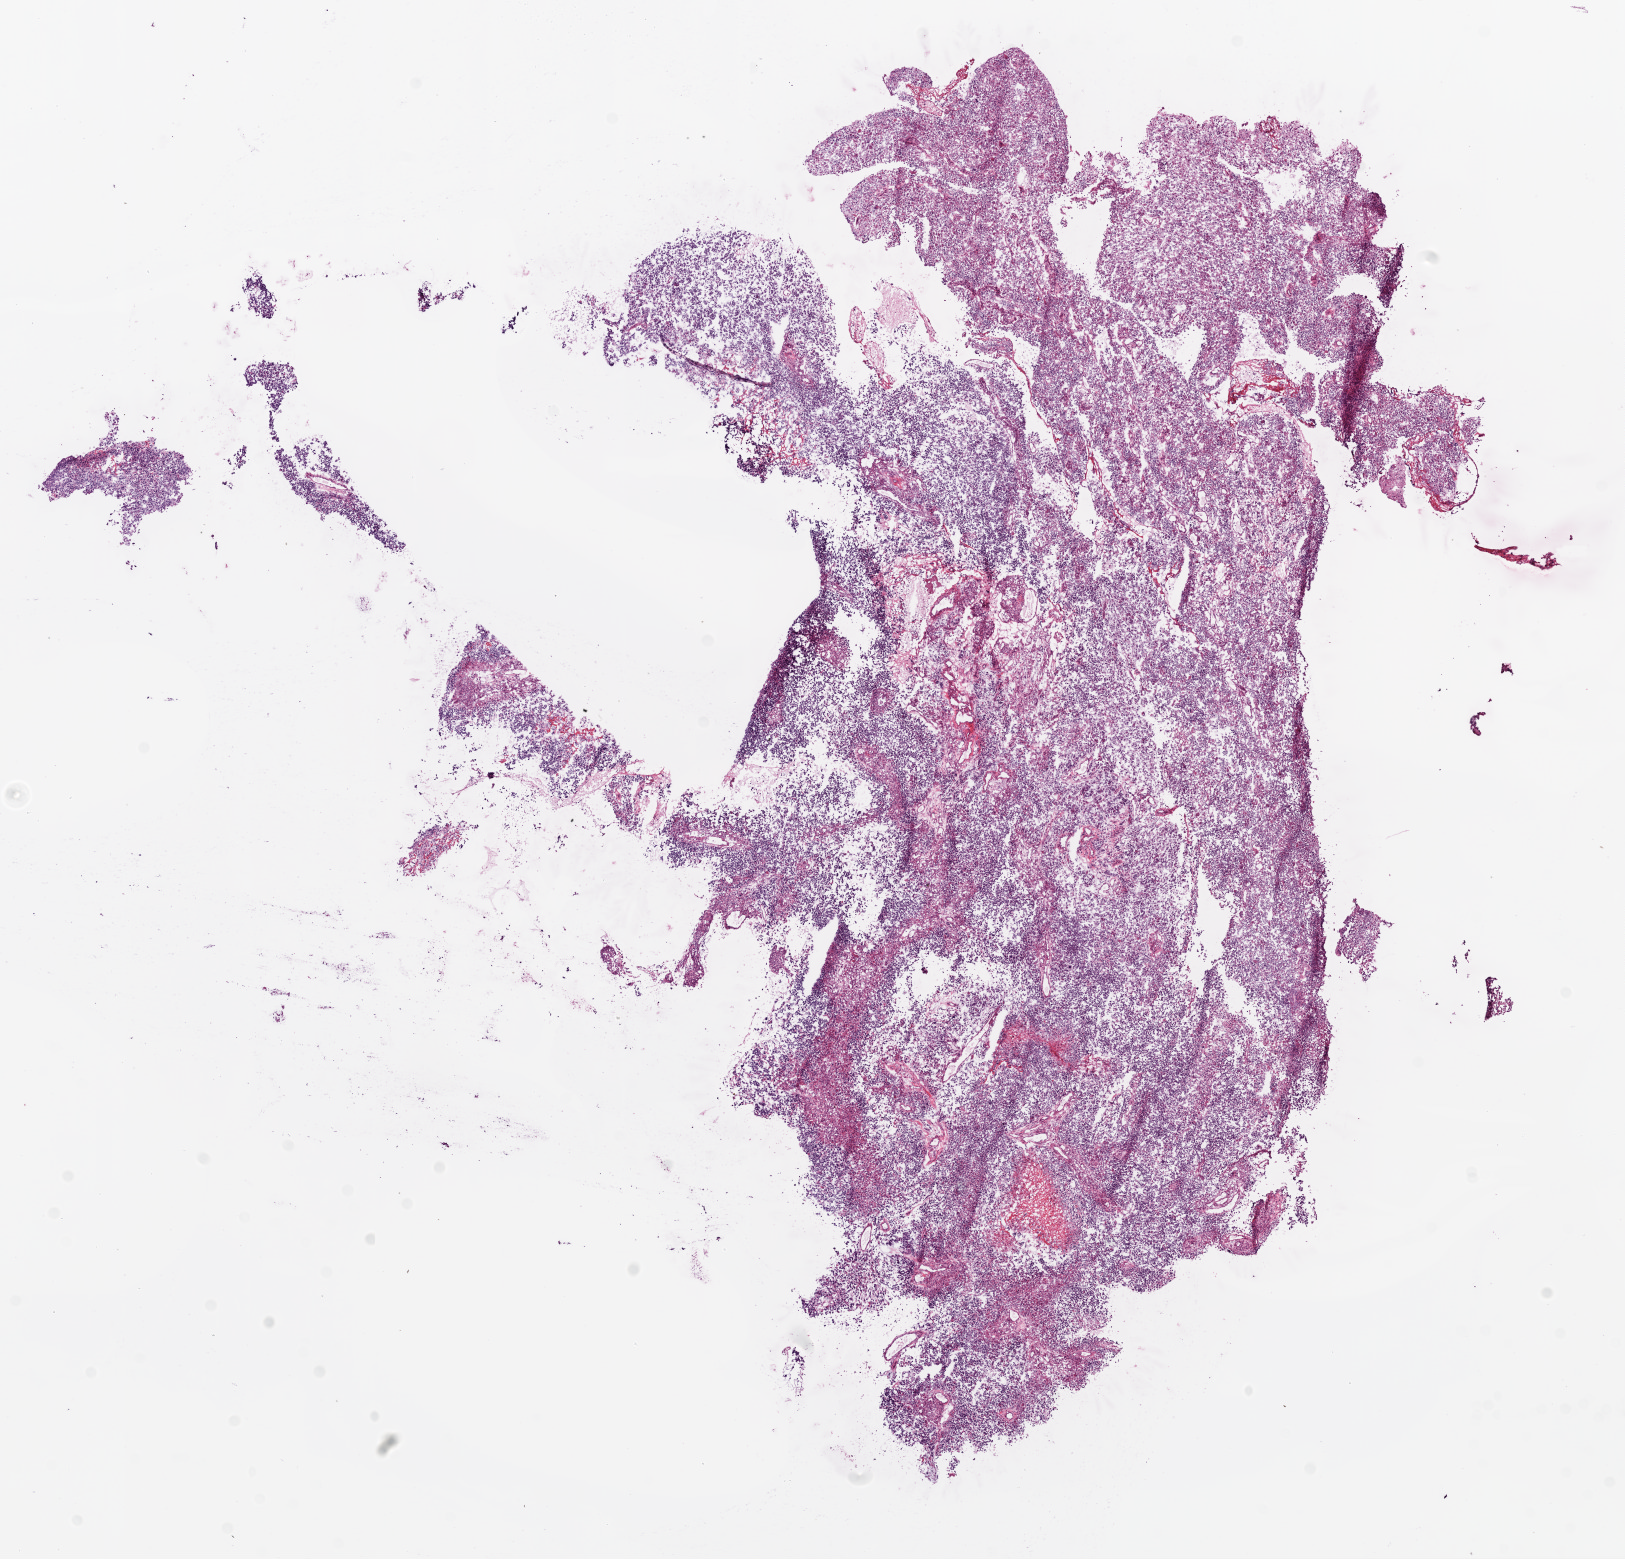
H&E-stained whole-slide image, a low-resolution overview of the entire scanned area, about 13.0 x 12.5 mm (slide scanned at 20x); frozen section; brain, primary tumour sample. Male, age 61 years at initial diagnosis. Composition of this section per pathologist review: tumour cells 90%, tumour nuclei 80%, normal cells 0%, stromal cells 0%, necrosis 10%.
Pathologic diagnosis: Glioblastoma.